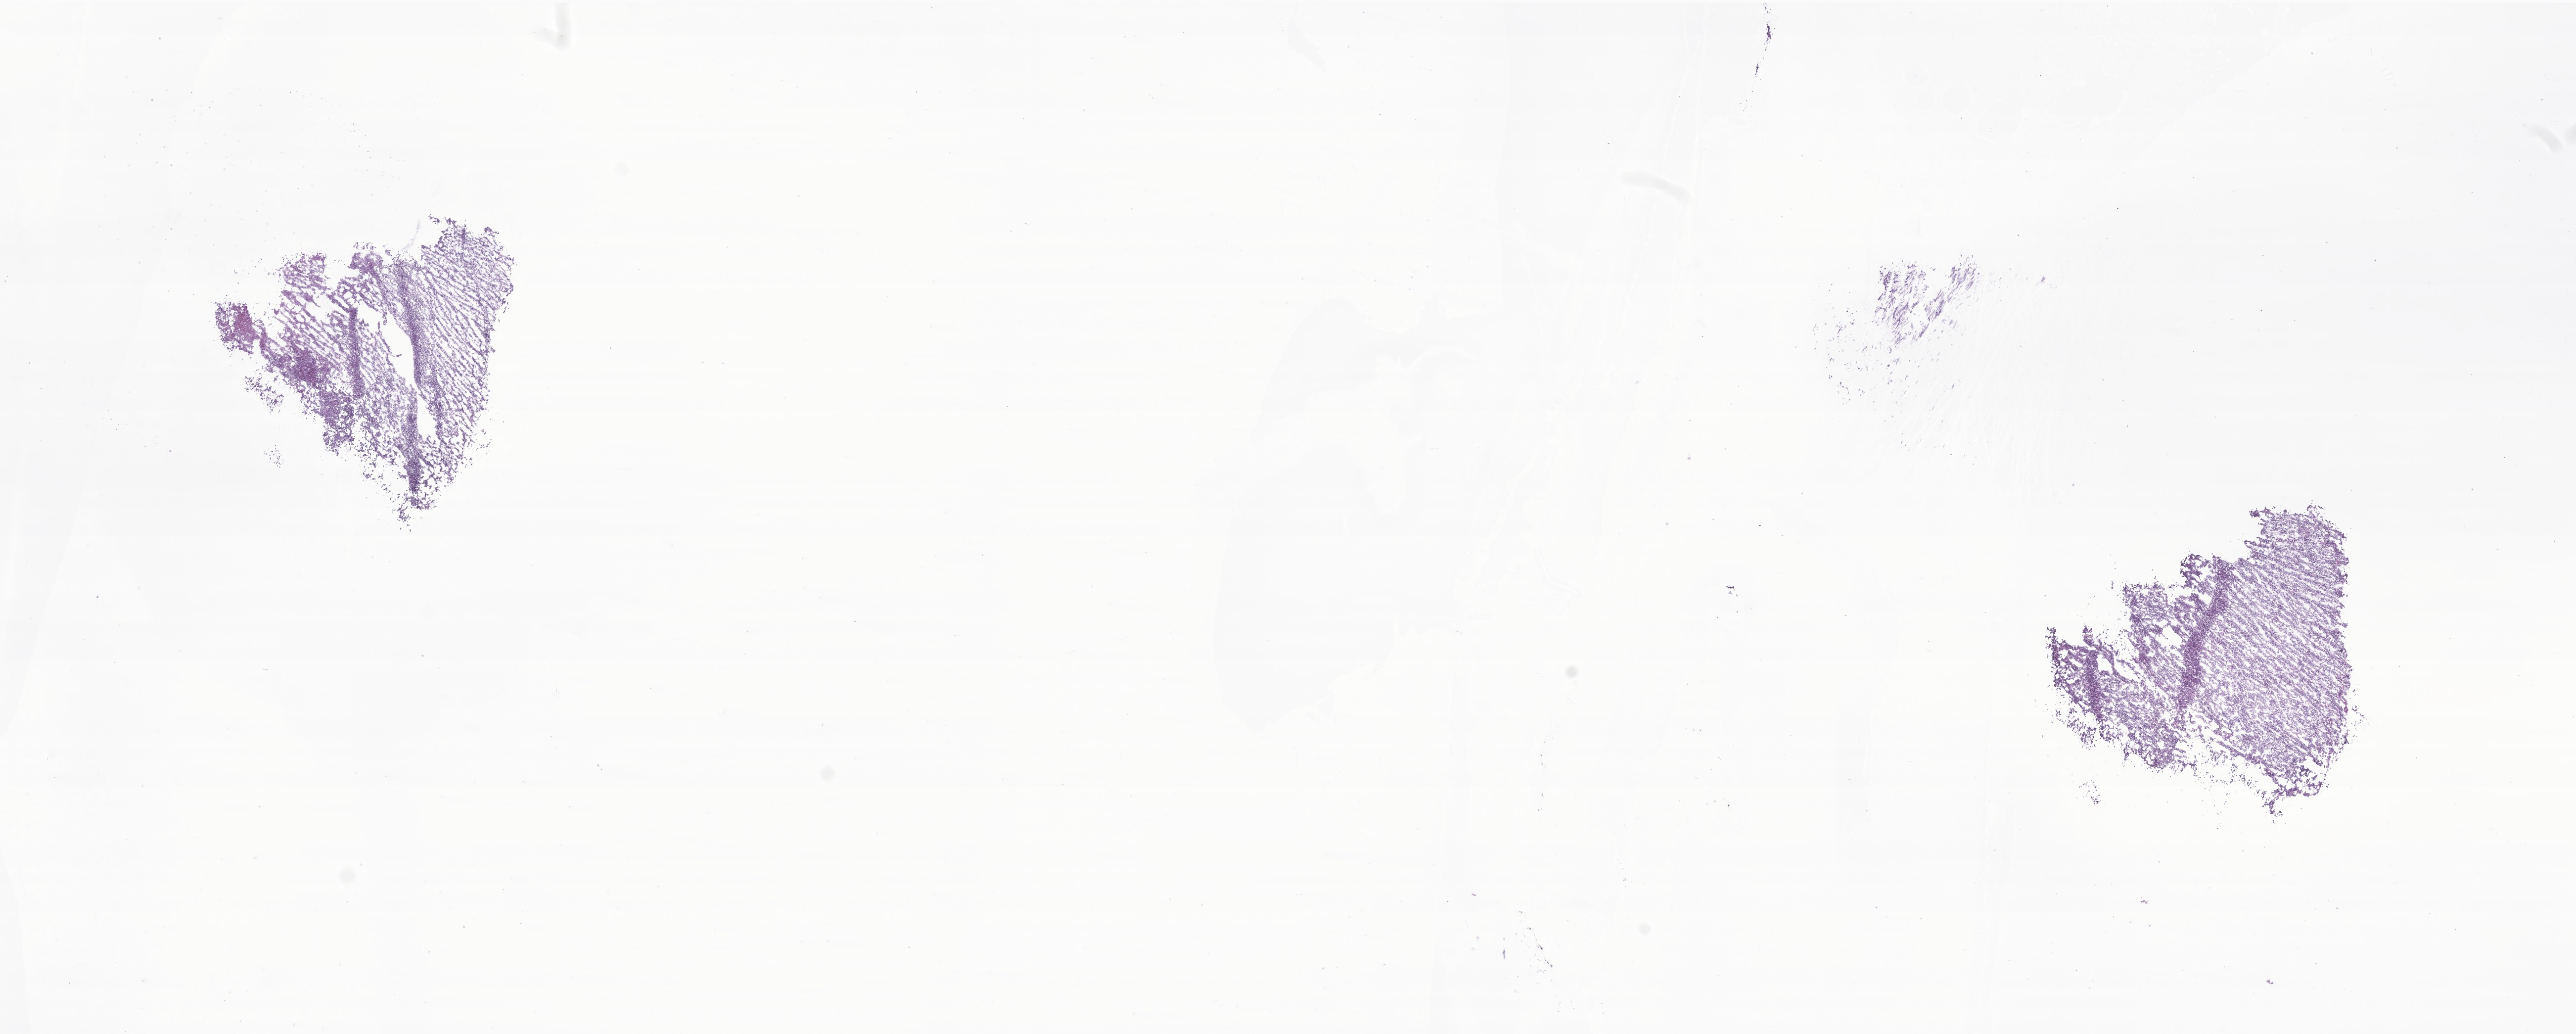
Digitized haematoxylin and eosin-stained section of tumor tissue from the cerebellum, shown as a low-resolution overview of the whole scanned area (about 22.0 x 8.8 mm); frozen section. Patient: male, age 120 months (10 years).
Diagnosis (ICD-O-3 morphology term): Medulloblastoma, NOS.